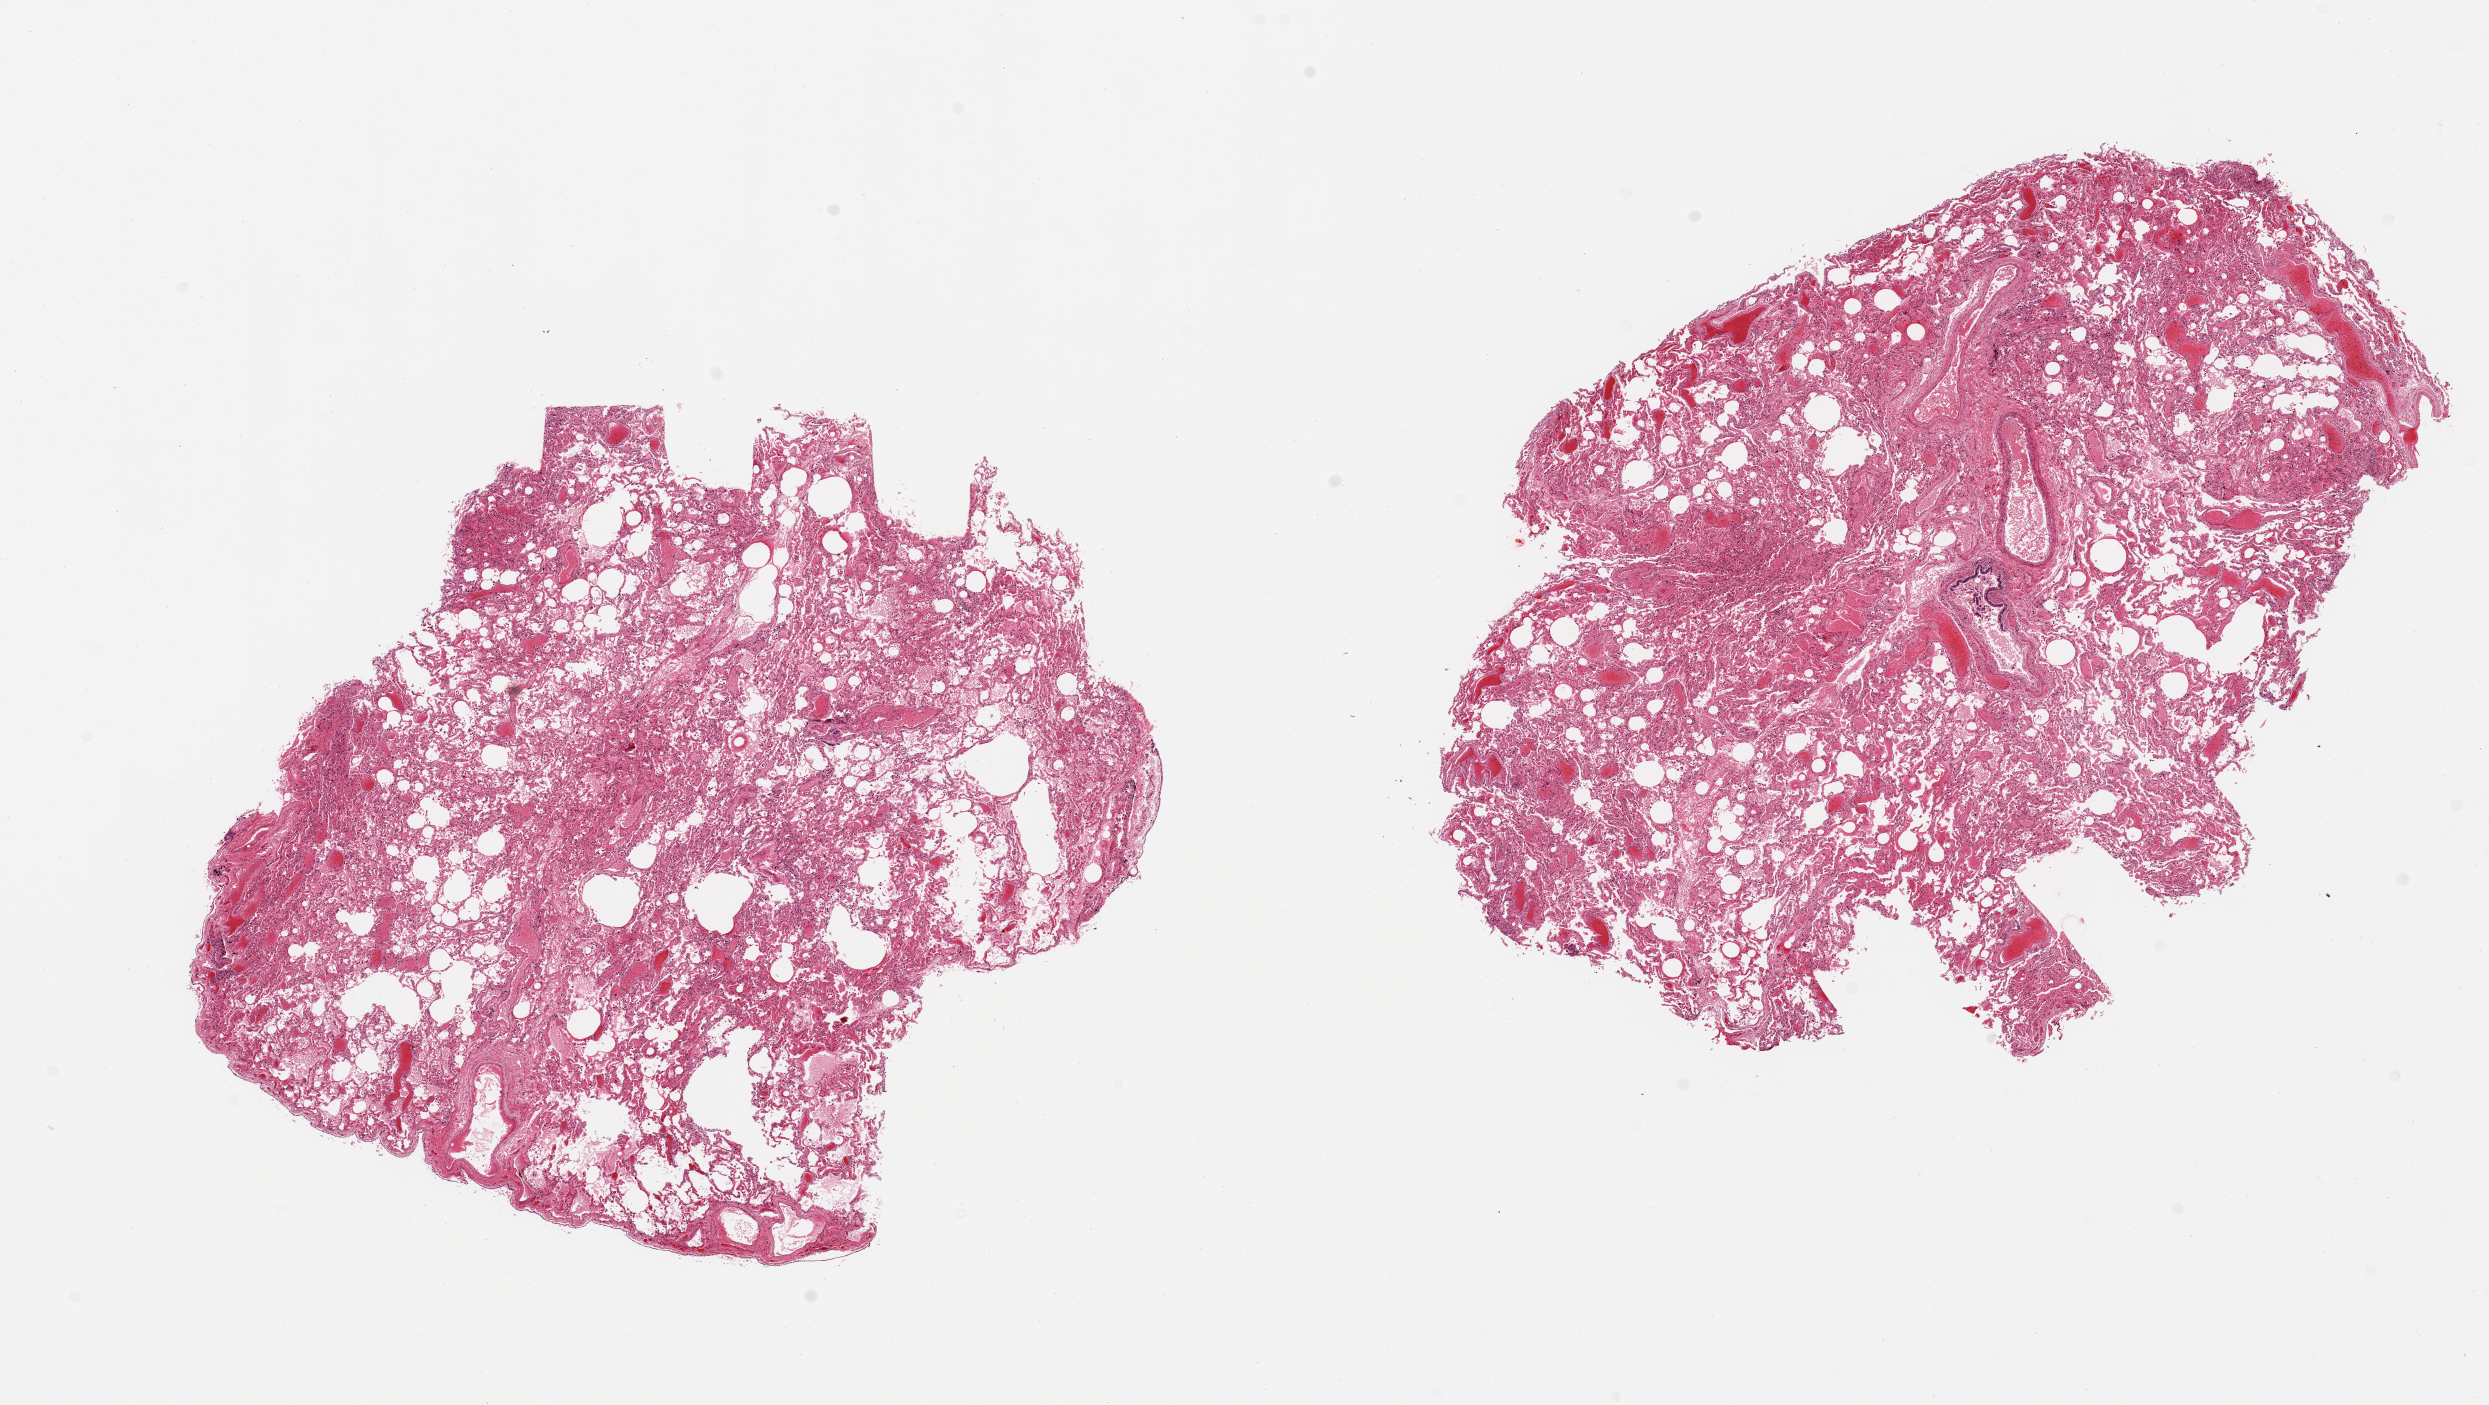
Digitized H&E-stained section, whole scanned area (about 19.7 x 11.1 mm, from a 20x scan) shown as a low-resolution overview, PAXgene-fixed paraffin-embedded (PFPE) section, sampled site (target tissue): lung, tissue donor sample. Donor sex: male.
Reviewer comment on this tissue sample: 2 pieces, moderate congestion/atalectasis.